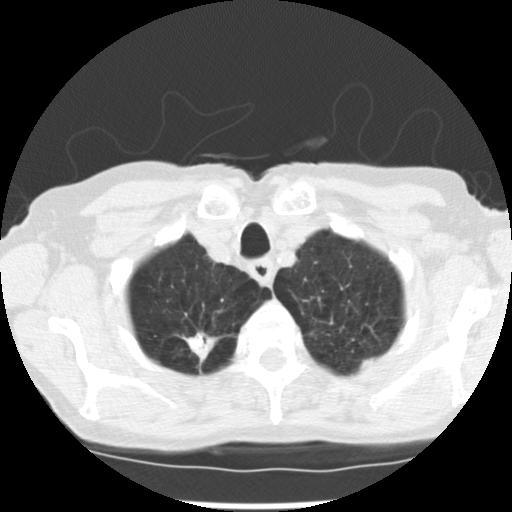
Low-dose screening chest CT, axial slice; baseline screening round; lung window (W 1500 / L -600 HU); 2.5 mm slice thickness; standard (soft-tissue) reconstruction kernel (STANDARD); slice 27 of 265 in the series. Female, age 72 years at enrolment. Current smoker at enrolment.
Lesion marked by an expert reader, box from (x=172, y=315) to (x=231, y=359) px. The screening reader recorded 3 non-calcified nodules or masses ≥4 mm on this exam (right upper lobe, left upper lobe, left lower lobe); which of them this box marks is not recorded. Official screen result: positive, change unspecified: nodule(s) >= 4 mm or enlarging nodule(s), mass(es), or other non-specific abnormalities suspicious for lung cancer.